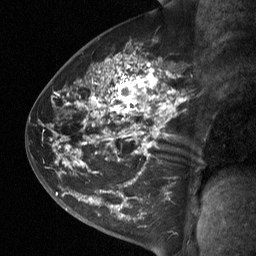
Breast MRI (dynamic contrast-enhanced), one sagittal slice. Position 39 of 64 along the scan axis. Dynamic contrast-enhanced study with each time point stored as its own series, time point 2 of 3 at this slice position (early post-contrast, ordered by acquisition time). 1.5 T. TE 4.8 ms, TR 27 ms. 2 mm slice thickness. 256 × 256 image matrix. Female patient, age 42 years. Case-level facts recorded for this patient, not image findings: setting: breast cancer imaged before/during neoadjuvant chemotherapy; receptor status: triple-negative.
Annotated regions visible in this slice (semi-automatic segmentation, software-assisted and operator-edited):
- analysis volume of interest (the breast-tissue region the enhancement analysis was run in; not a lesion): bounding box [x1, y1, x2, y2] px = [49, 45, 198, 197]
- tumour enhancement mask (voxels above the 90 % enhancement threshold inside the analysis volume of interest): [66, 57, 178, 167]